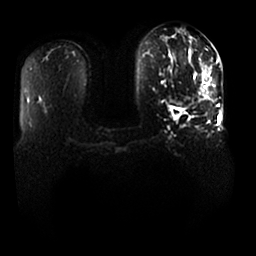
Breast MRI, one axial slice; slice 8 of 25 in the series (ordered by position); diffusion-weighted series; image 2 of 4 stored at this slice position (different b-values; order by instance number); 1.5 T; 4 mm slice thickness; 256 × 256 image matrix, field of view 370 × 370 mm. Female patient.
Annotated regions visible in this slice (outlined manually by an expert reader):
- tumour on diffusion-weighted imaging: bounding box (x1, y1, x2, y2) in pixels: (171, 68, 211, 104)